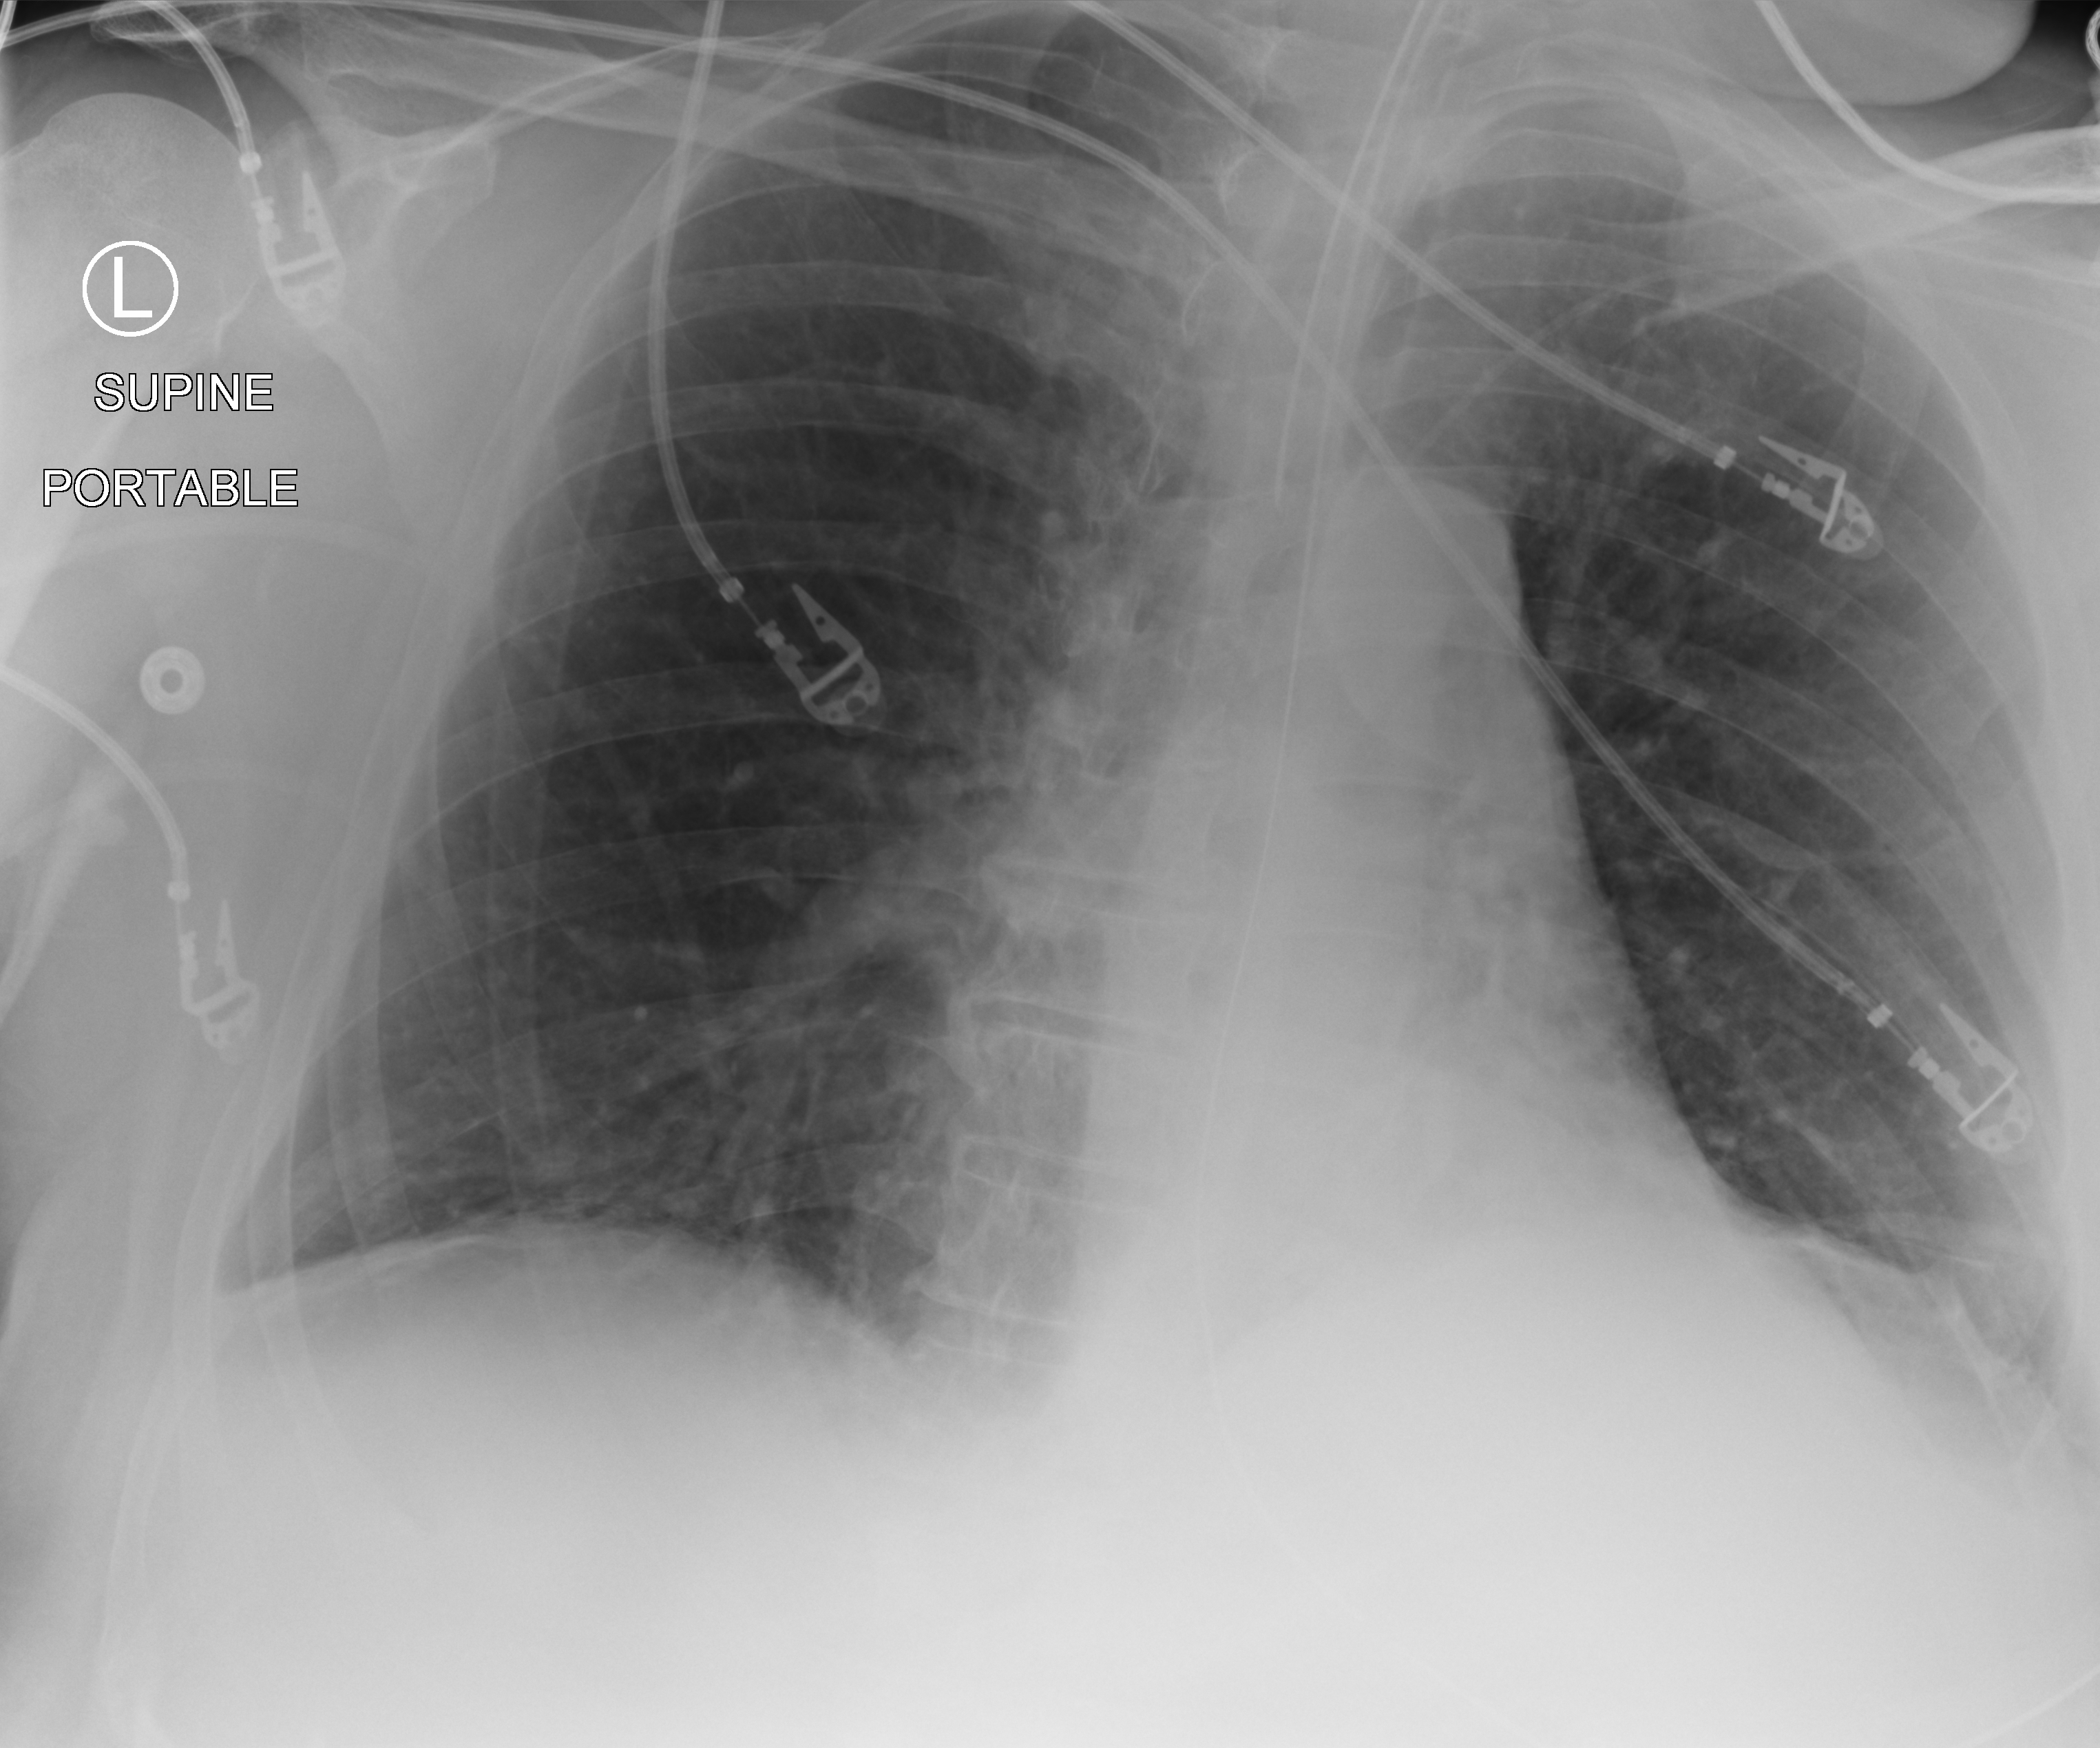
Portable chest radiograph, anteroposterior (AP) projection. Male patient hospitalised with COVID-19, age 60–74 years.
Admission-level facts for this patient (not findings on this image; timing relative to this image not recorded):
- mechanically ventilated during this hospital stay: yes
- length of hospital stay: 22 days